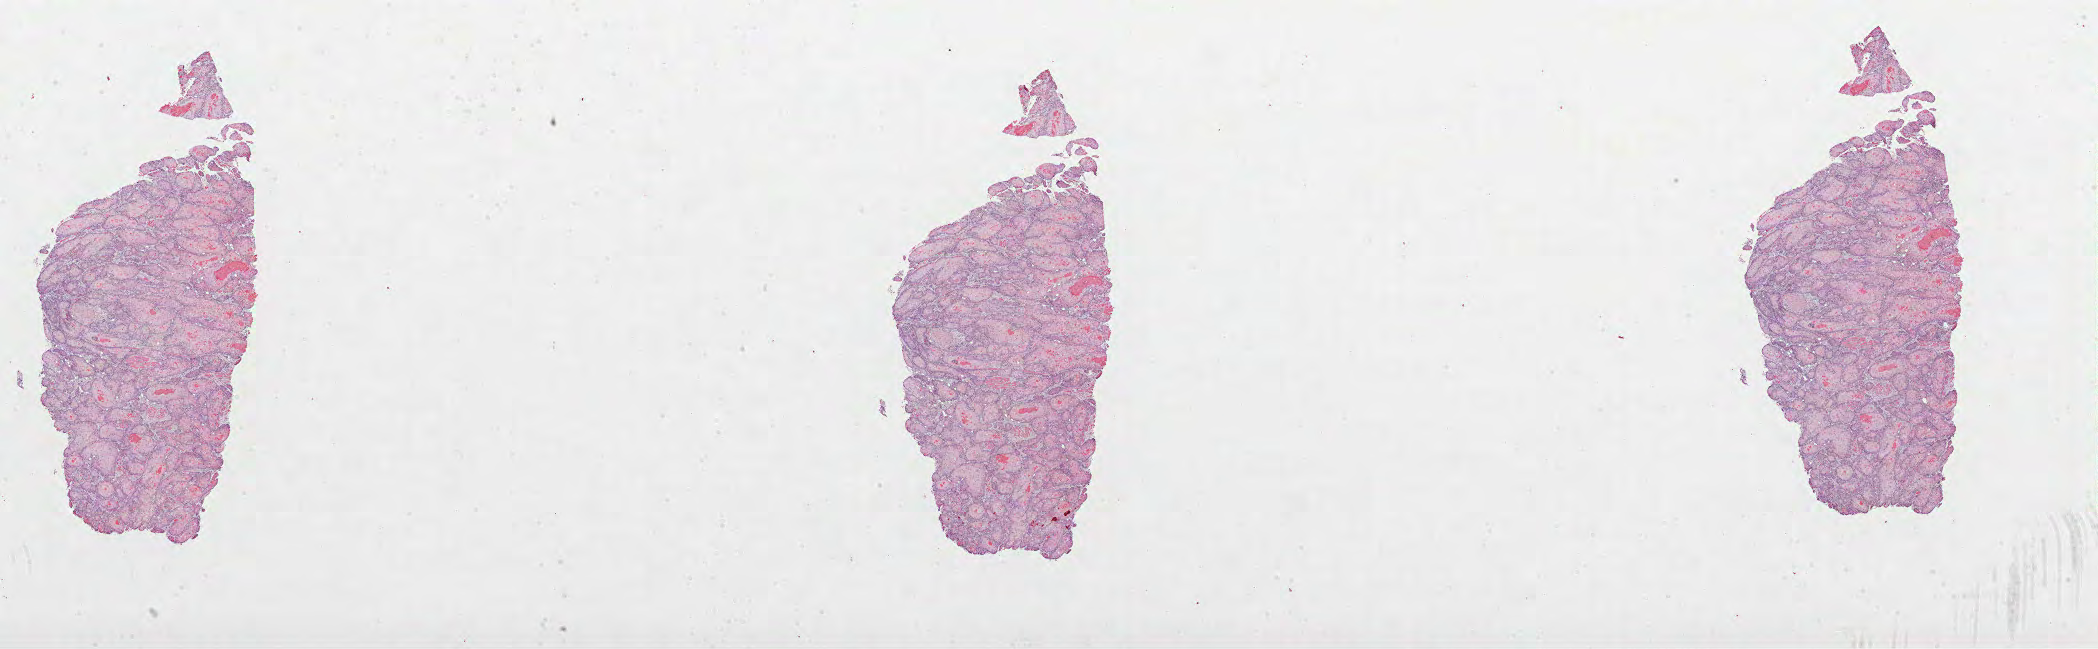
Digitized Hematoxylin and eosin (H&E) stained tissue section (whole slide) — shown as a low-resolution overview of the whole scanned area (about 33.8 x 10.5 mm, acquisition: 40x scan); formalin-fixed paraffin-embedded (FFPE) diagnostic section; head and neck, primary tumour sample. Female patient; age at initial diagnosis 70 years. Histologic grade: G2 (moderately differentiated).
- histologic diagnosis: Squamous cell carcinoma, NOS (tongue, NOS)